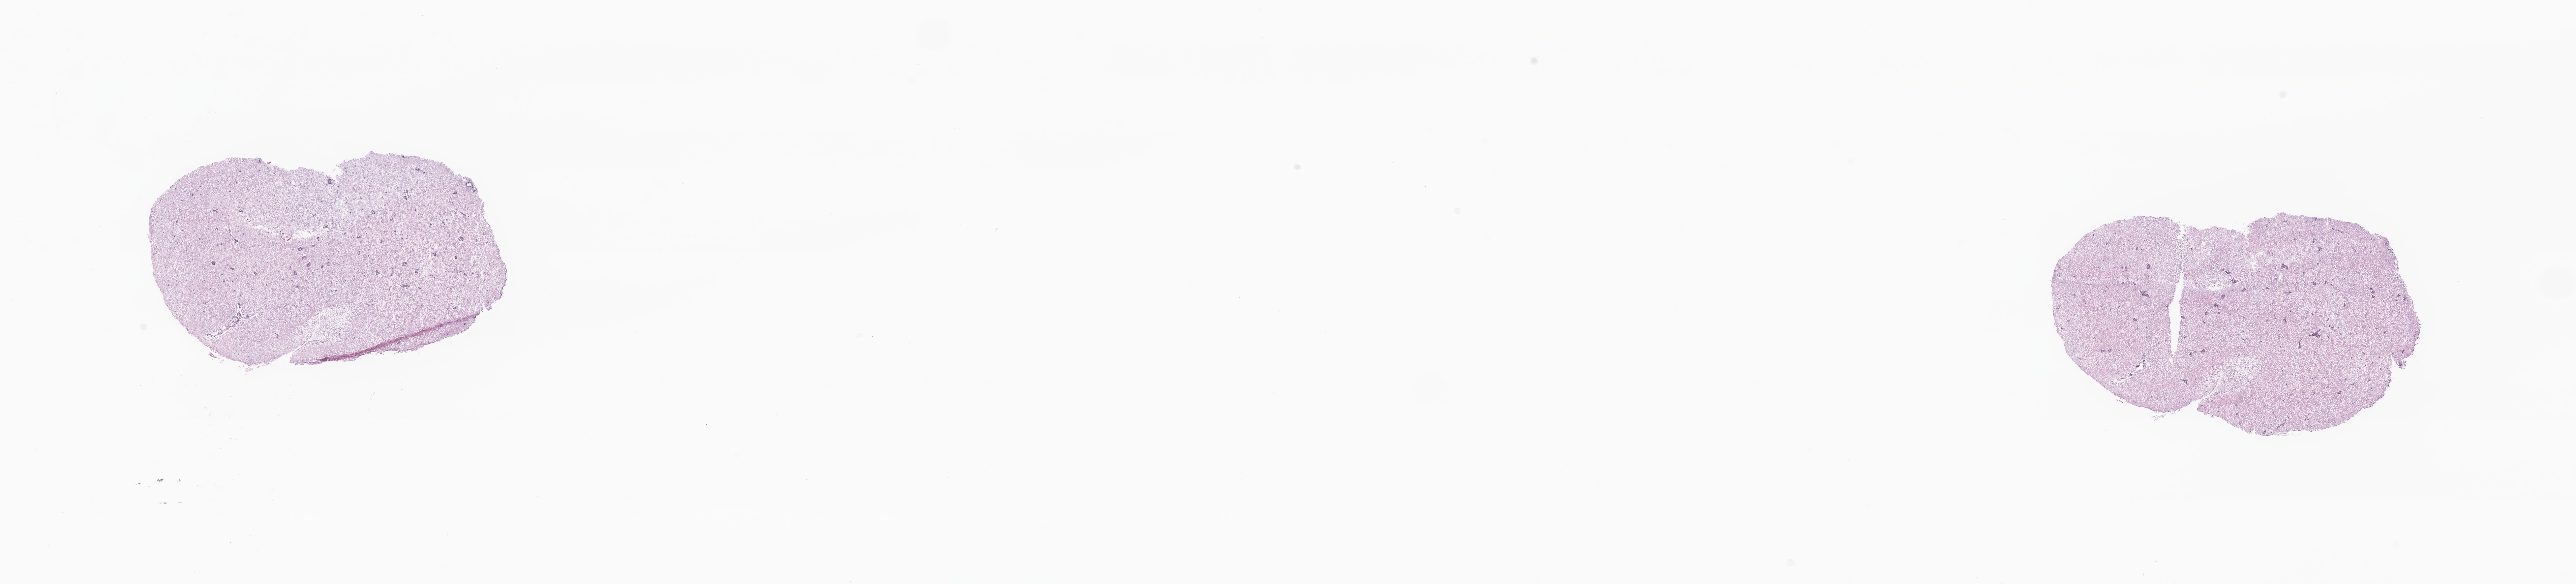
Whole-slide image, haematoxylin and eosin stain of tumor tissue from the brain — low-resolution overview of the scanned area, about 32.9 x 7.5 mm, frozen section (OCT-embedded). Patient: male, age 77 months (6 years 5 months).
• diagnosis: Glioma, malignant